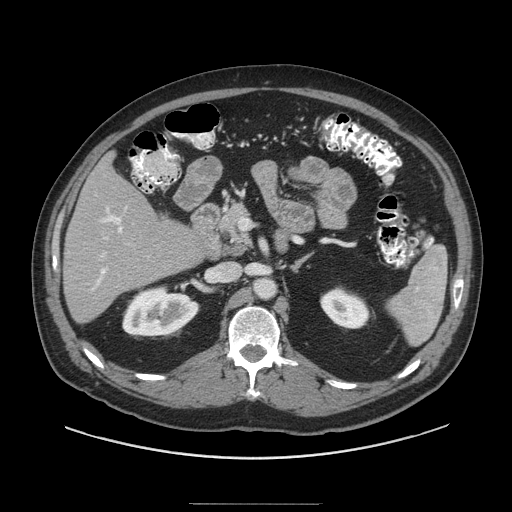
Contrast-enhanced abdominal CT (liver protocol), one axial slice. Slice 46 of 91 in the series (ordered by position). Reconstruction kernel STANDARD. 140 kVp. Soft-tissue window (W 400 / L 40 HU). 2.5 mm slice thickness. 512 × 512 image matrix, field of view 440 × 440 mm. From the clinical record (not read from this slice): diagnosis: hepatocellular carcinoma (patient treated with transarterial chemoembolisation; whether this scan precedes or follows treatment is not stated here); TNM stage (as recorded): Stage-I; Child-Pugh class: A; tumour differentiation: well differentiated; tumour nodularity: uninodular.
Structures marked on this image (semi-automatic segmentation, software-assisted and operator-edited):
- liver parenchyma outside the tumour (the mass and vessels are separate outlines, so this box may not span the whole liver): box from (x=62, y=154) to (x=206, y=322) px
- liver vessels: (x=92, y=206)–(x=127, y=290)